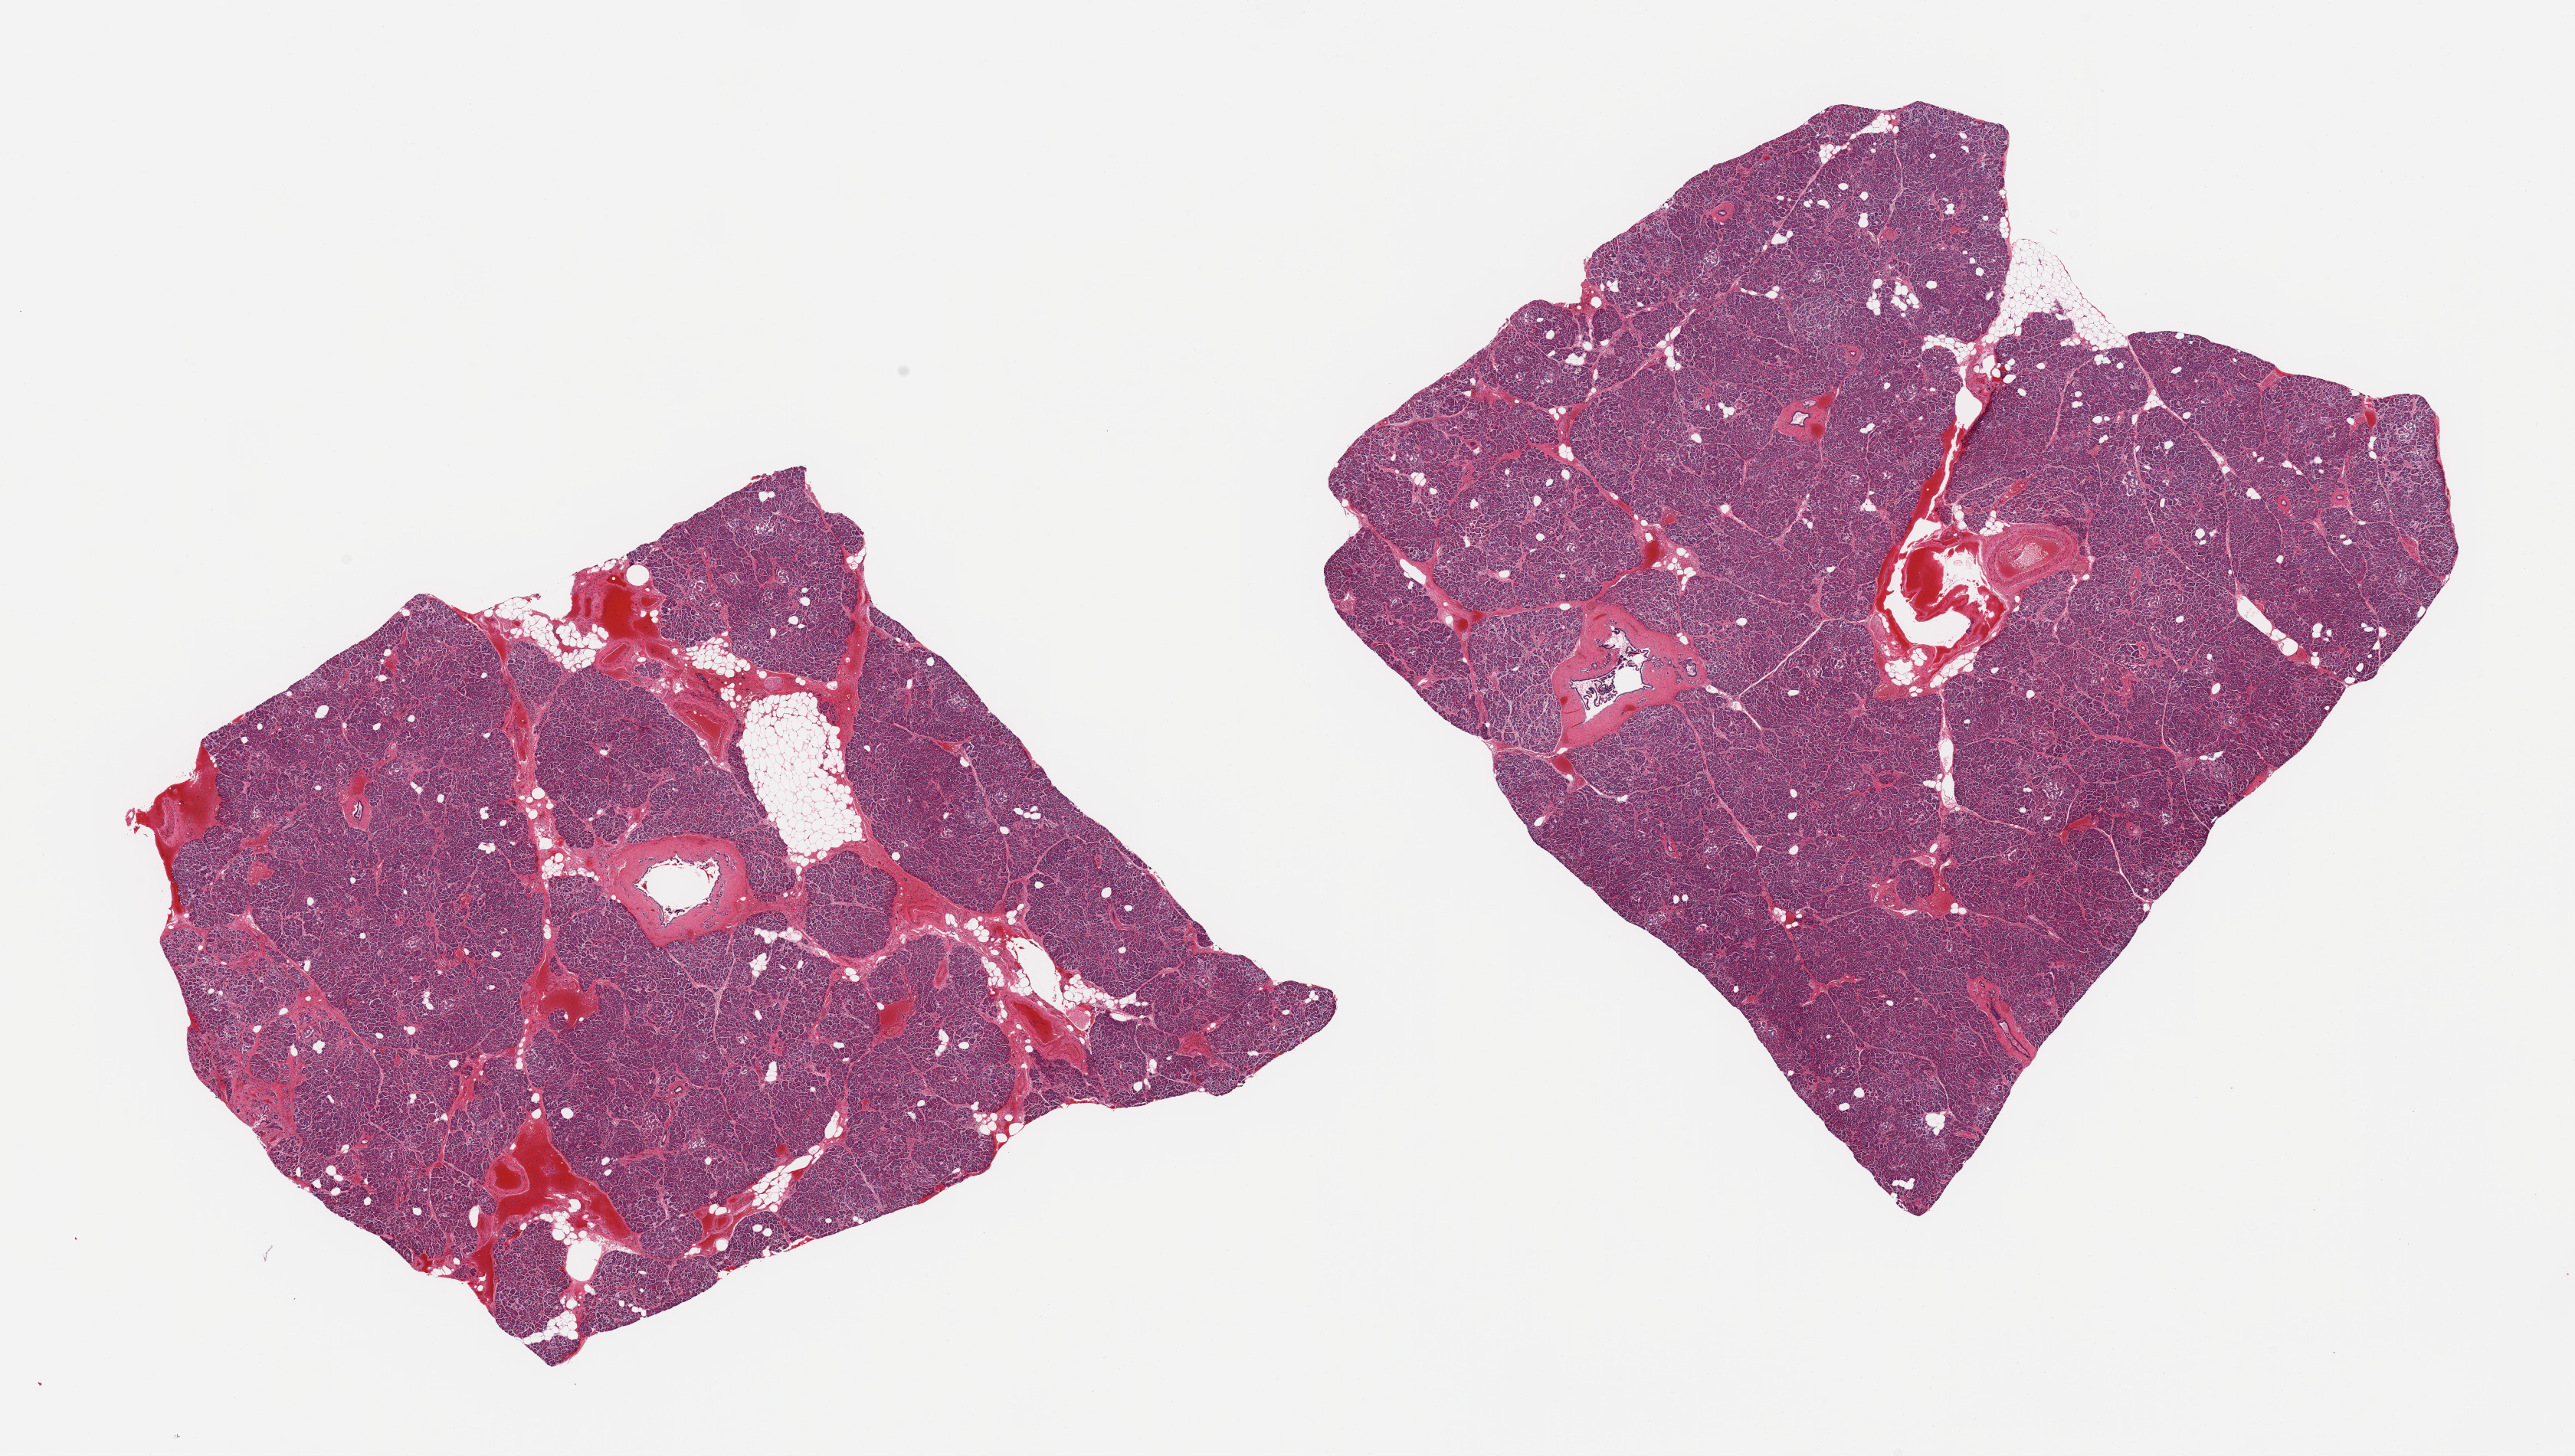
Digitized hematoxylin and eosin (H&E)-stained section — whole scanned area (about 26.6 x 15.0 mm) shown as a low-resolution overview, PAXgene-fixed paraffin-embedded (PFPE) section, sampled site (target tissue): pancreas, tissue donor sample. Female donor.
Reviewer comment on this tissue sample: 2 pieces, moderate saponification; Islets visible, early degenerative changes.